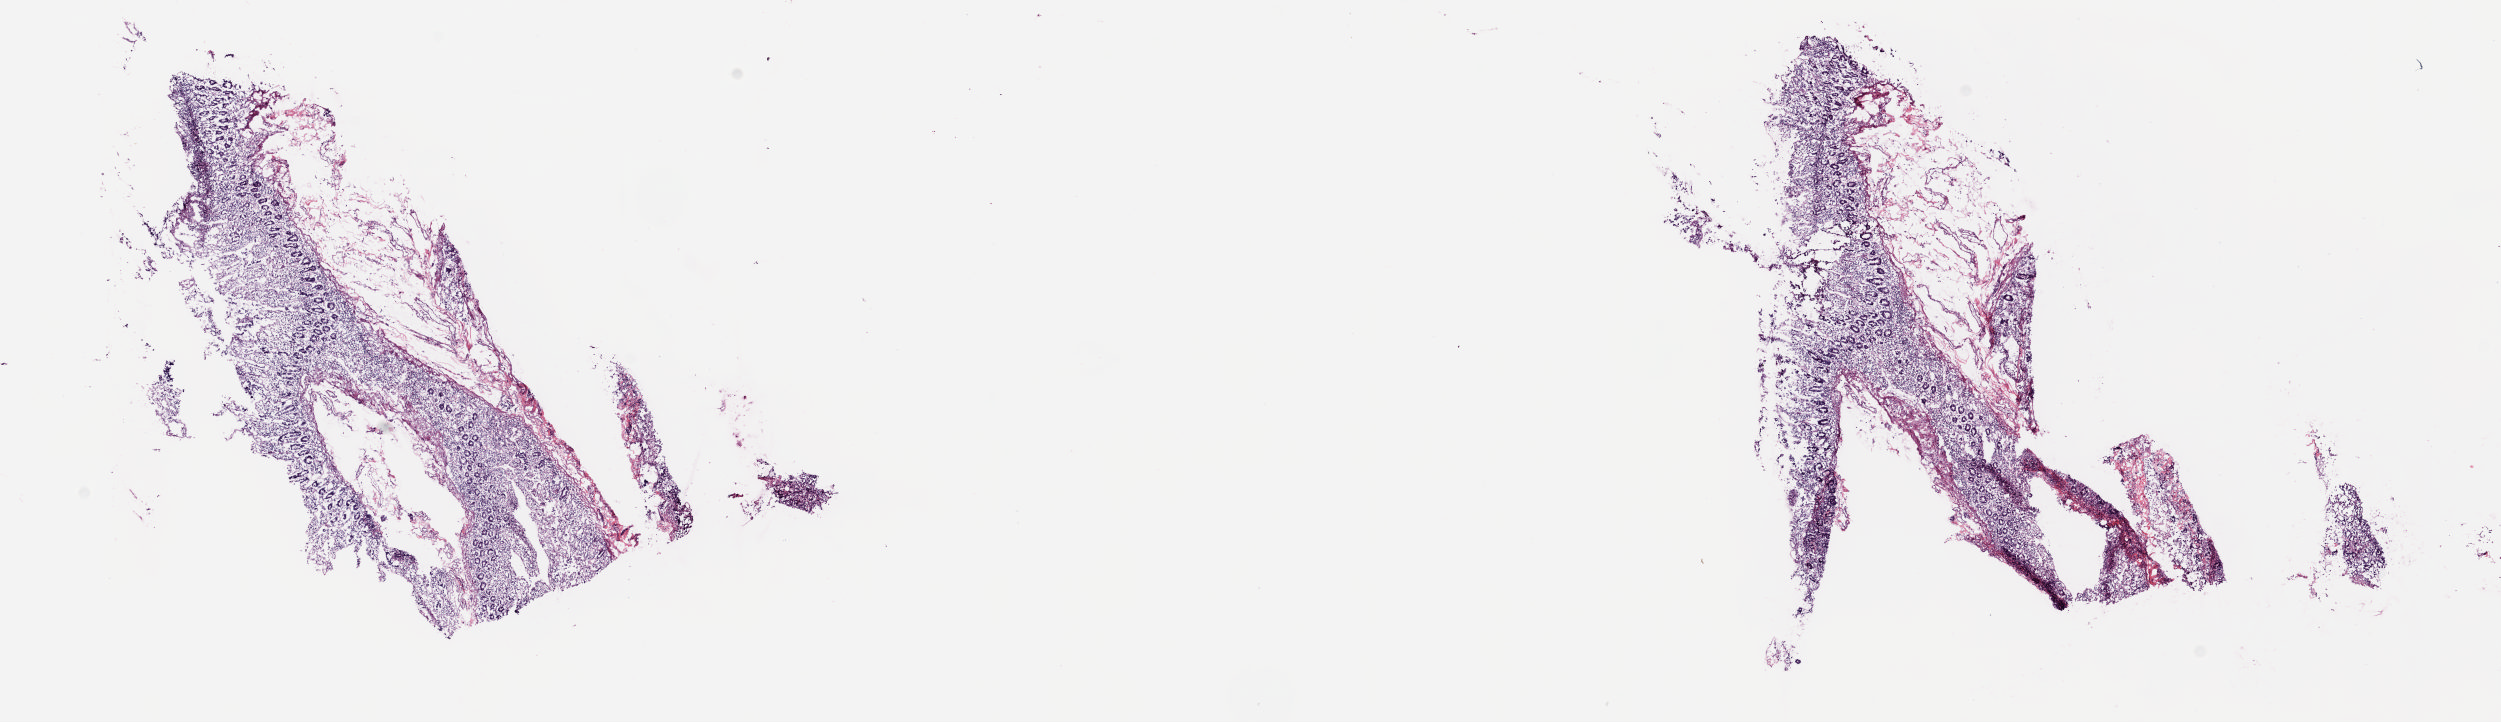
Whole-slide histology image, H&E, a low-resolution overview of the entire scanned area, about 19.8 x 5.7 mm, frozen section, sample: solid tissue normal (non-tumour tissue), pancreas. Male, age 73 years at initial diagnosis. Composition of this section per pathologist review: tumour cells 0%, tumour nuclei 0%, normal cells 20%, stromal cells 80%, necrosis 0%. Inflammatory infiltration, as recorded: lymphocyte infiltration 35%, monocyte infiltration 3%, neutrophil infiltration 3%.
• this section: solid tissue normal (non-tumour) sample from the same patient
• patient diagnosis: Adenocarcinoma, NOS (head of pancreas)